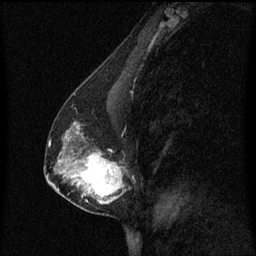
Breast MRI (dynamic contrast-enhanced), one sagittal slice. Position 32 of 60 along the scan axis. Dynamic contrast-enhanced series, image 2 of 3 at this slice position (ordered by acquisition). 1.5 T. TE 4.2 ms, TR 8.4 ms. 256 × 256 image matrix, field of view 200 × 200 mm. Female patient, age 40 years. Case-level facts recorded for this patient, not image findings: setting: breast cancer imaged before/during neoadjuvant chemotherapy; receptor status: triple-negative.
Annotated regions visible in this slice (semi-automatic segmentation, software-assisted and operator-edited):
- analysis volume of interest (the breast-tissue region the enhancement analysis was run in; not a lesion): bounding box [x1, y1, x2, y2] px = [60, 120, 131, 215]
- tumour enhancement mask (voxels above the 70 % enhancement threshold inside the analysis volume of interest): [66, 126, 123, 205]